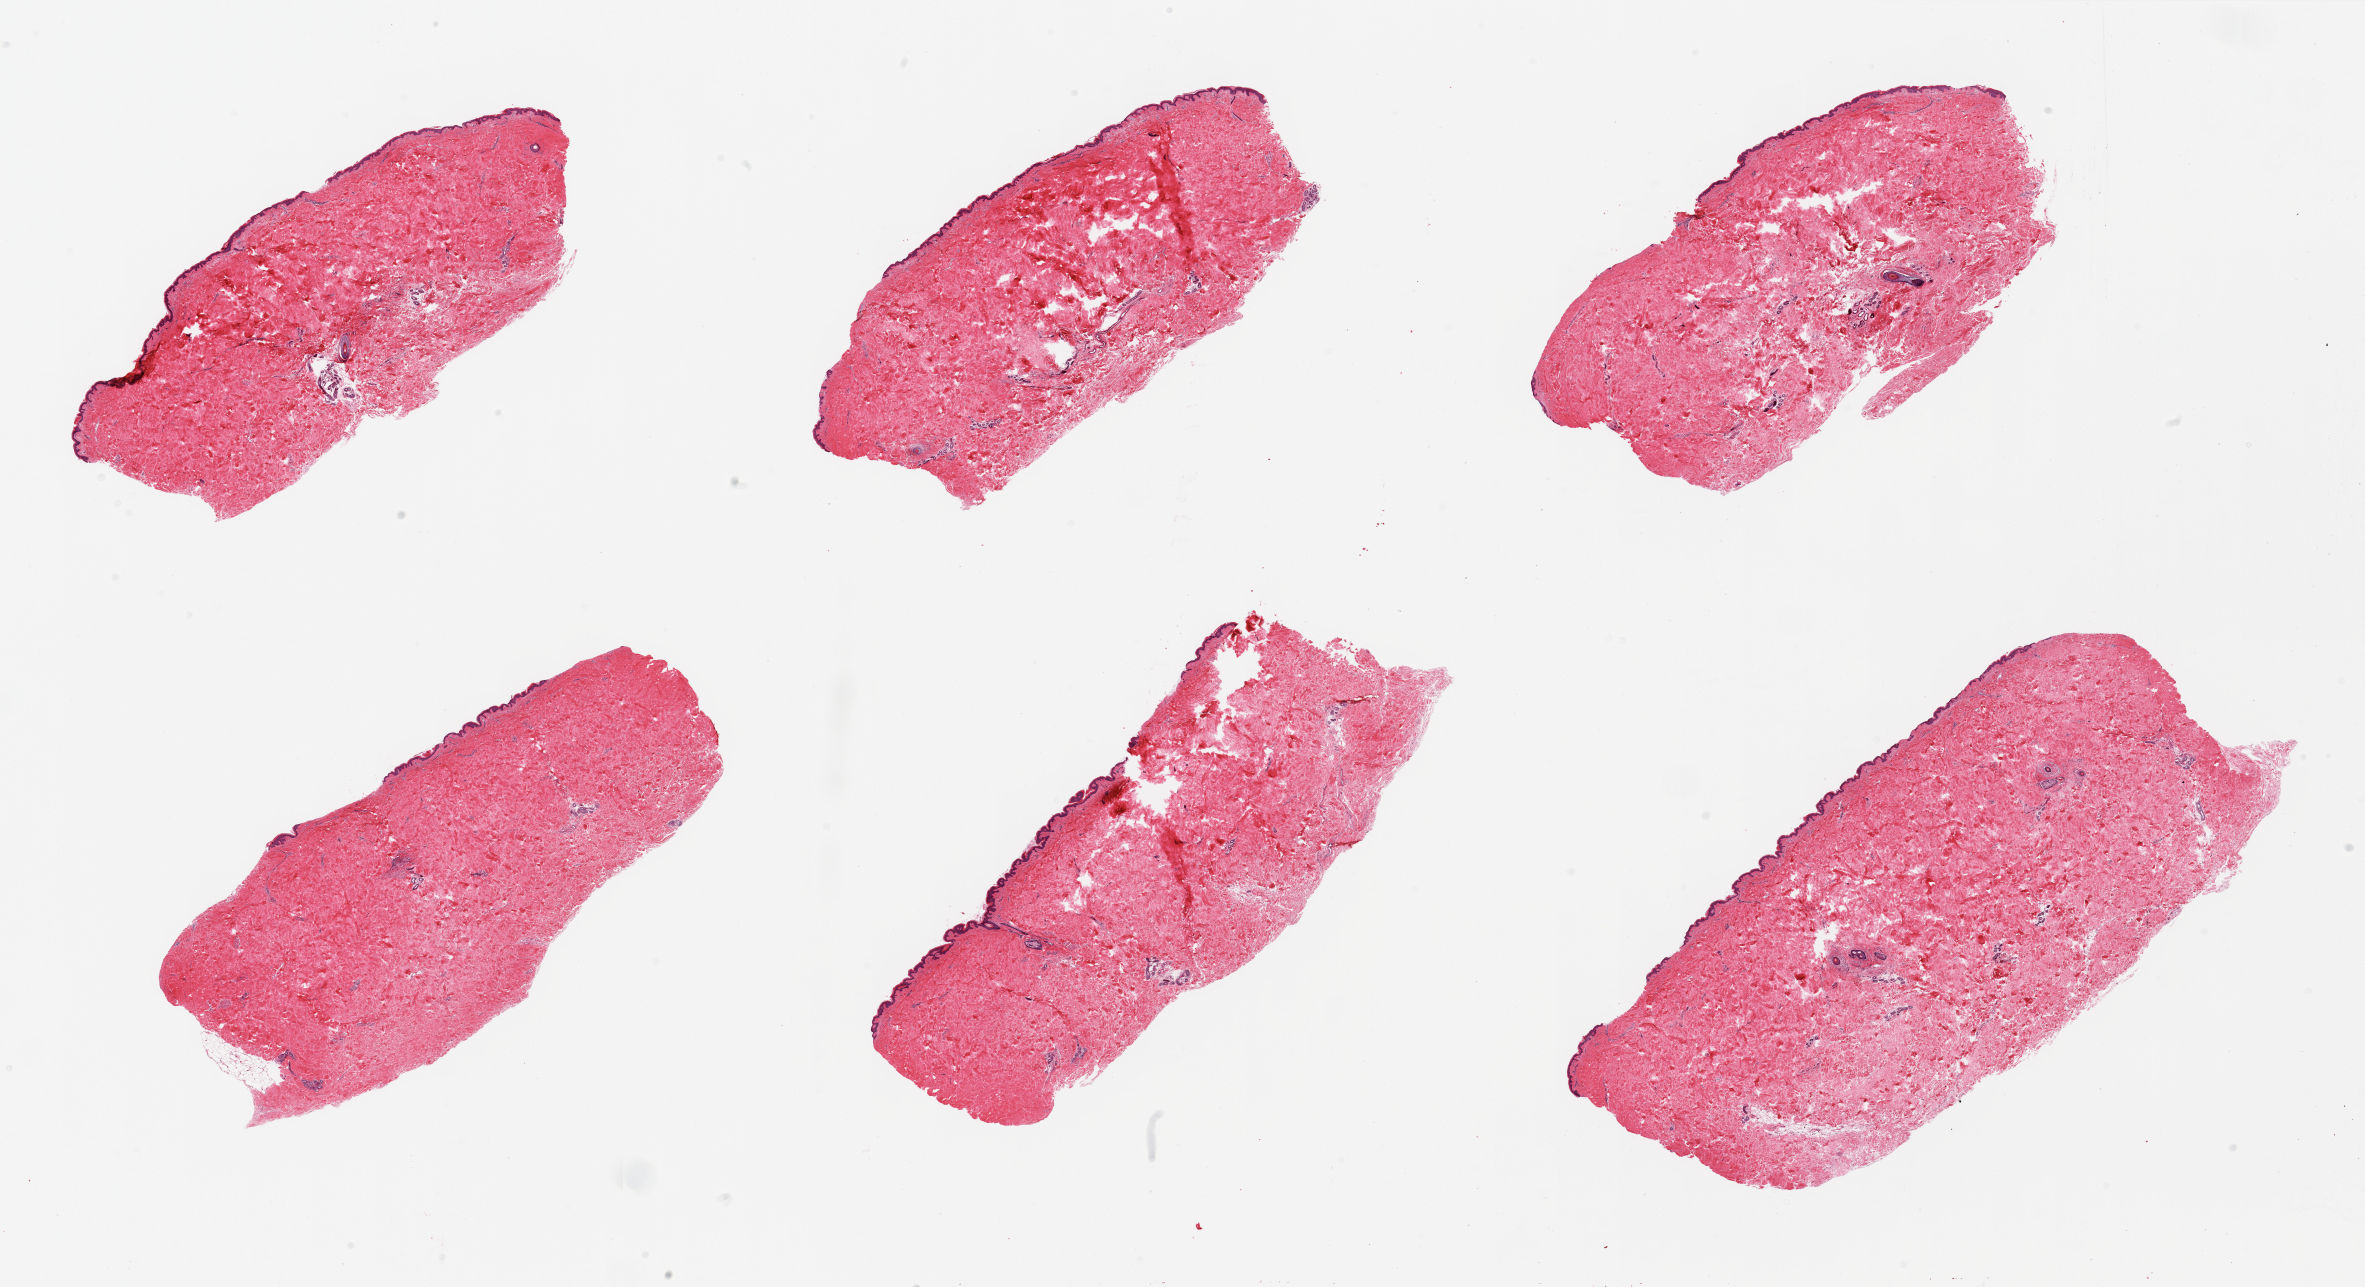
Digitized H&E-stained section — shown as a low-resolution overview of the whole scanned area (about 37.4 x 20.4 mm, slide scanned at 20x); PAXgene-fixed, paraffin-embedded tissue; sampled site (target tissue): skin of suprapubic region; tissue donor sample. Donor sex: female.
- reviewer comment on this tissue sample: 6 pieces, minimal dermal fat, squamous epithelium is ~30 microns